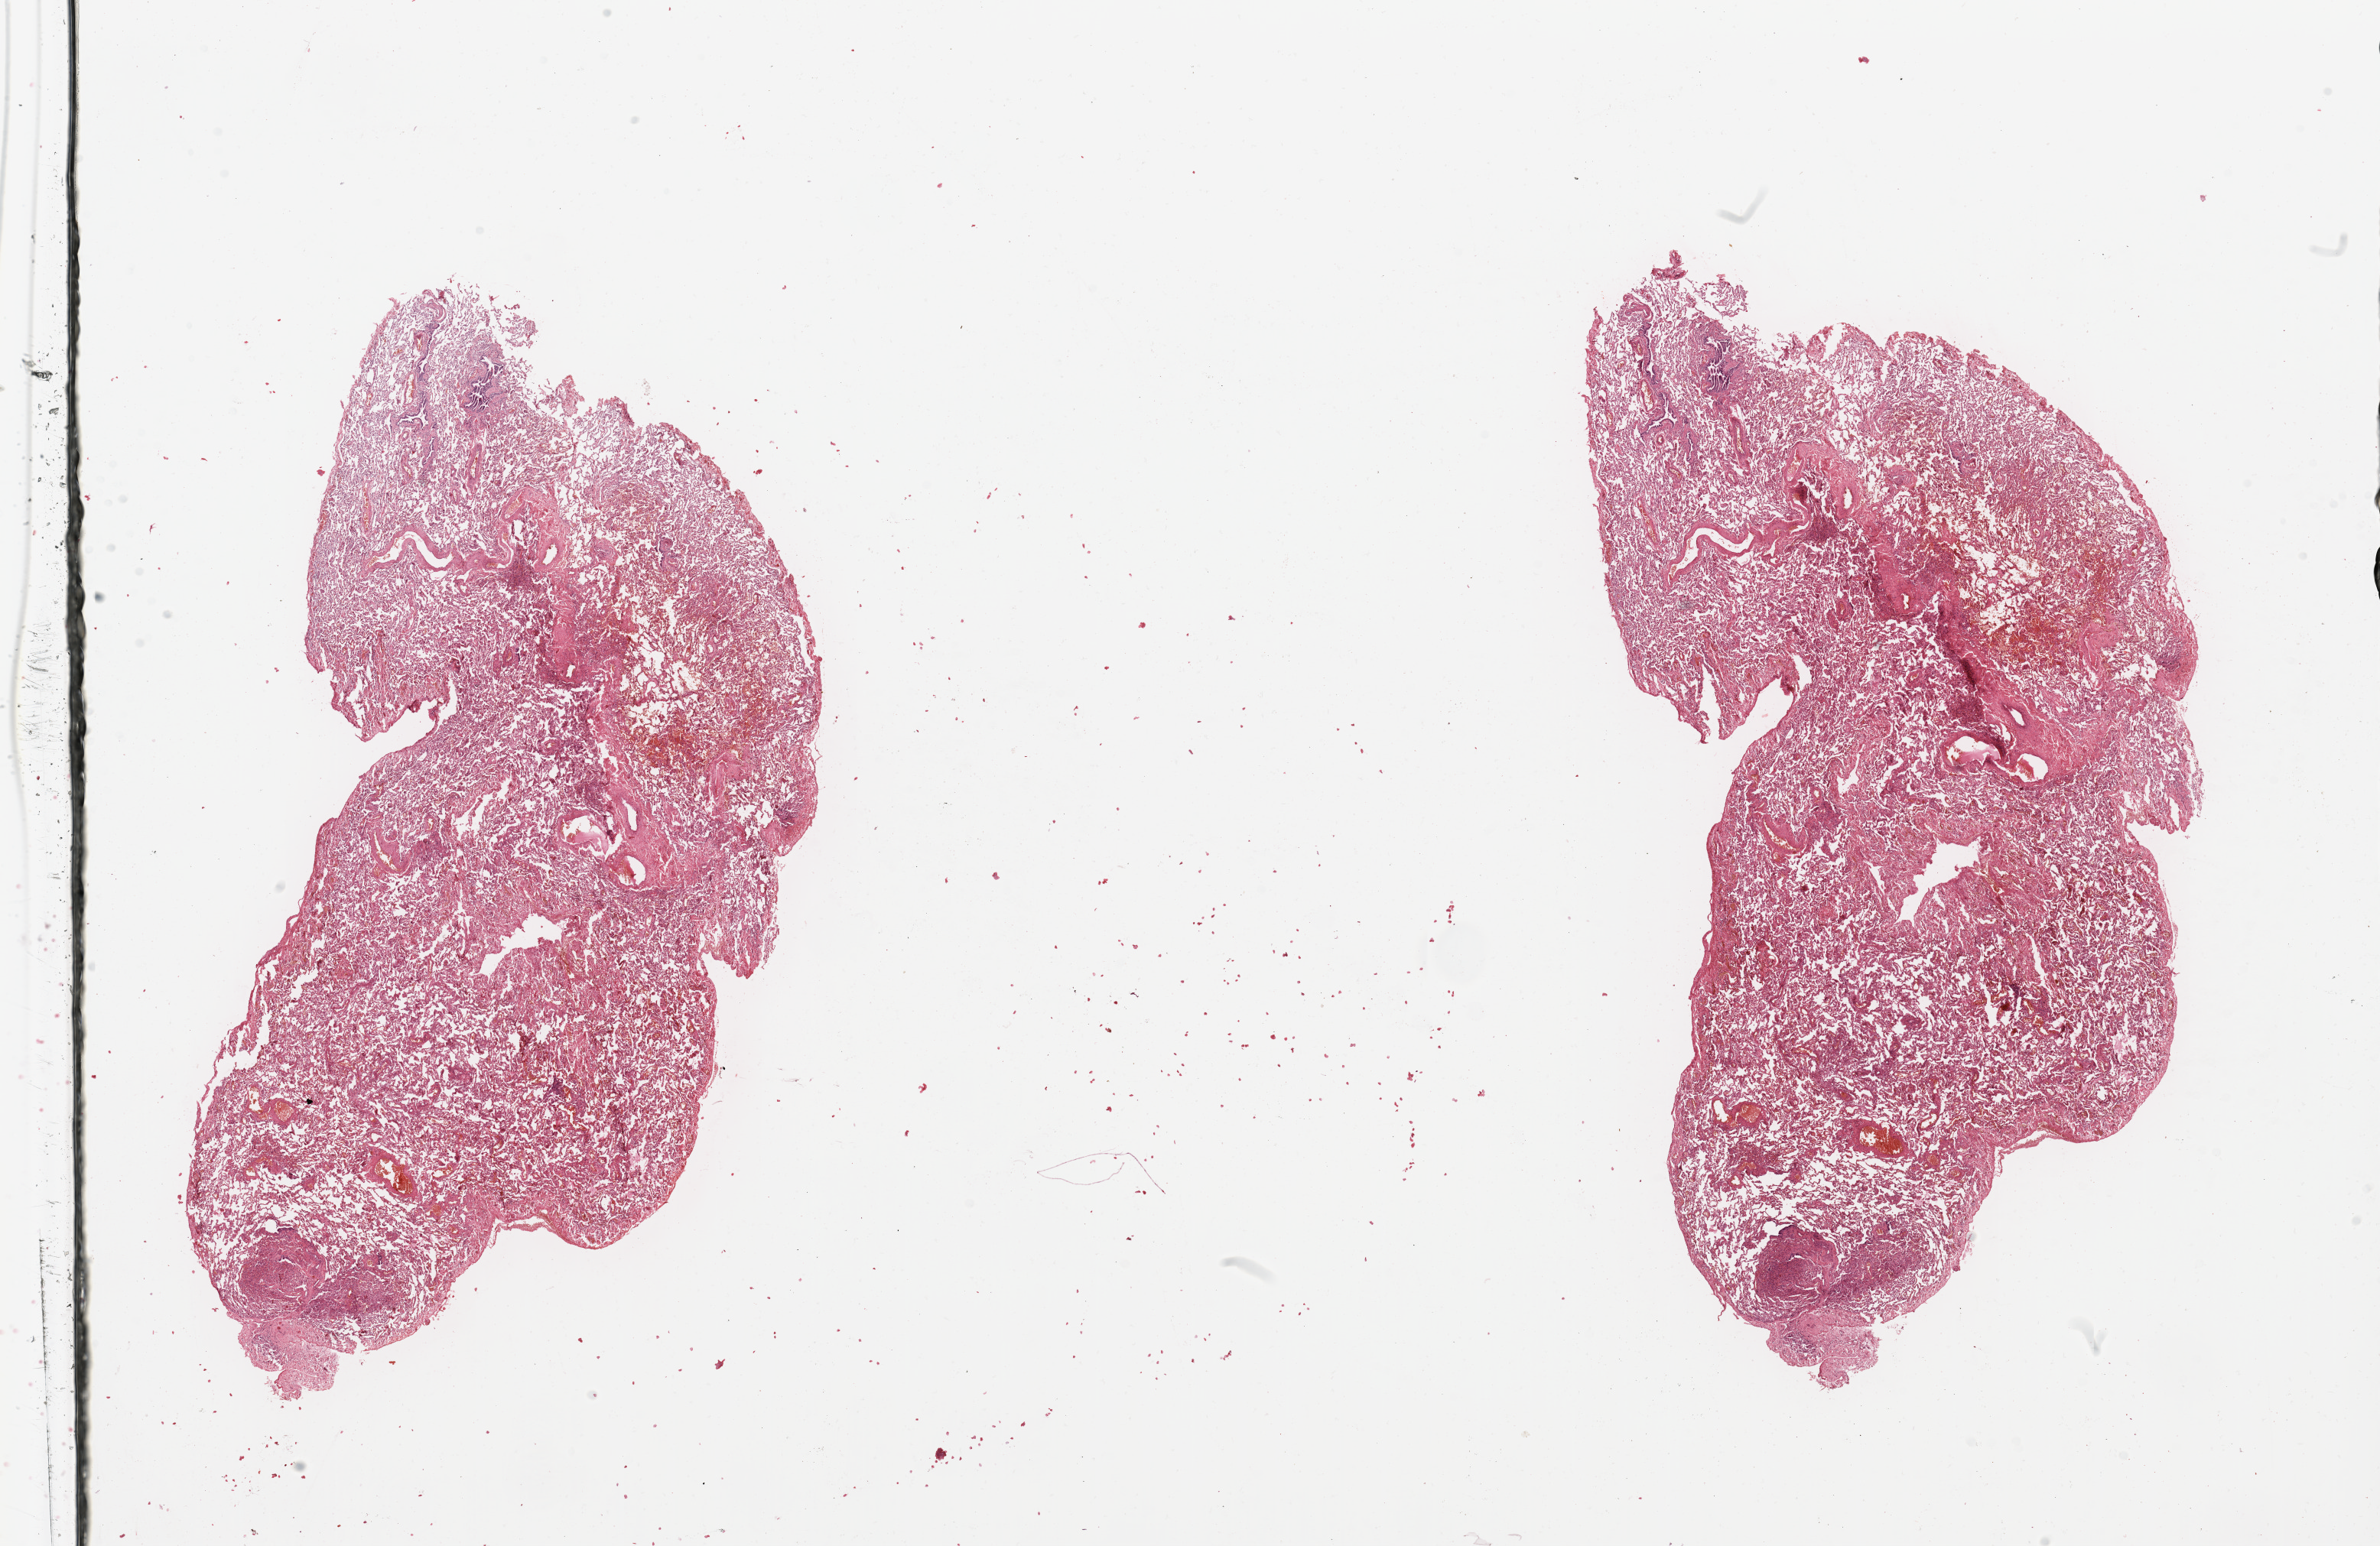
Whole-slide histology image, H&E-stained, whole scanned area (about 24.6 x 16.0 mm, slide scanned at 20x) shown as a low-resolution overview. Normal (non-tumour) tissue sample, sampled site: lung. Patient: female, age 36 years.
This section: normal (non-tumour) tissue from the same patient. Patient diagnosis: Adenocarcinoma, NOS.